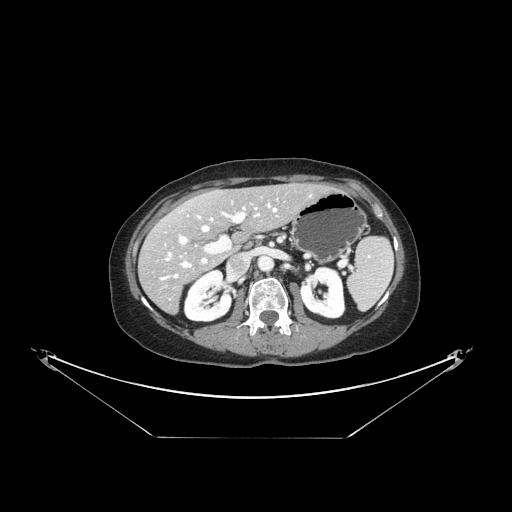
Contrast-enhanced abdominal CT, one axial slice; slice 82 of 148 in the series (ordered by position); reconstruction kernel STANDARD; 120 kVp; intravenous contrast given; soft-tissue window (W 400 / L 40 HU); 512 × 512 image matrix, field of view 500 × 500 mm. Female patient, age 73 years. From the clinical record (not read from this slice): diagnosis: colorectal cancer liver metastases, imaged before liver resection; multiple liver metastases: no; largest metastasis: 1 cm; disease in both lobes: no.
Annotated regions visible in this slice (expert manual segmentation):
- hepatic veins: bounding box [x1, y1, x2, y2] px = [161, 204, 277, 280]
- liver: [140, 184, 329, 313]
- planned liver remnant (the part of the liver to remain after resection): [168, 184, 328, 240]
- portal vein (with intrahepatic branches): [179, 204, 257, 264]